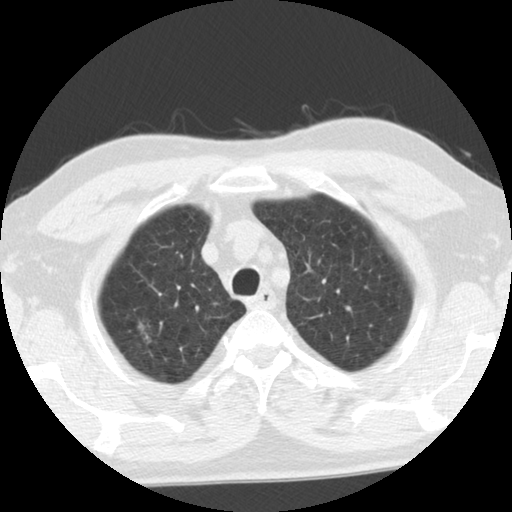
Chest CT (low-dose screening protocol), one axial image, second screening round (one year after baseline), lung window (W 1500 / L -600 HU), standard (soft-tissue) reconstruction kernel (STANDARD). Male participant, aged 68 years at enrolment. Former smoker at enrolment.
- Expert reader's lesion annotation, bounding box [x1, y1, x2, y2] px = [127, 315, 161, 354].
- The exam's reader record, not a measurement of the box and not confirmed to be the same lesion: non-calcified nodule or mass ≥4 mm, right upper lobe, poorly defined margins, ground glass attenuation, pre-existing on the prior screen: yes; interval growth: yes.
- Official screen result: positive, other.
- Later outcome: lung cancer diagnosed 88 days after this screen — adenocarcinoma, NOS, right upper lobe, moderately differentiated (G2), stage IA (AJCC 6th edition), 28 mm at pathology.